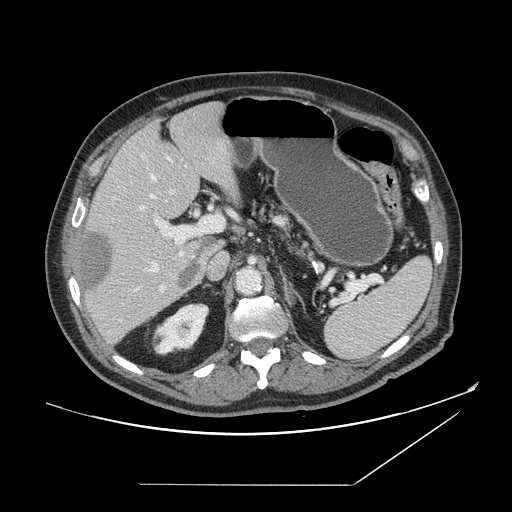
Contrast-enhanced abdominal CT, one axial slice; slice 97 of 166 in the series (ordered by position); intravenous contrast given; soft-tissue window (W 400 / L 40 HU); 512 × 512 image matrix, field of view 416 × 416 mm. Male patient, age 80 years. From the clinical record (not read from this slice): diagnosis: colorectal cancer liver metastases, imaged before liver resection; multiple liver metastases: no; largest metastasis: 2.2 cm; chemotherapy before resection: no.
Outlined on this slice (outlined manually by an expert reader):
- hepatic veins: bounding box (x1, y1, x2, y2) in pixels: (135, 175, 173, 292)
- liver: (78, 102, 243, 345)
- planned liver remnant (the part of the liver to remain after resection): (93, 102, 242, 255)
- portal vein (with intrahepatic branches): (141, 206, 225, 291)
- liver metastasis: (82, 232, 200, 298)